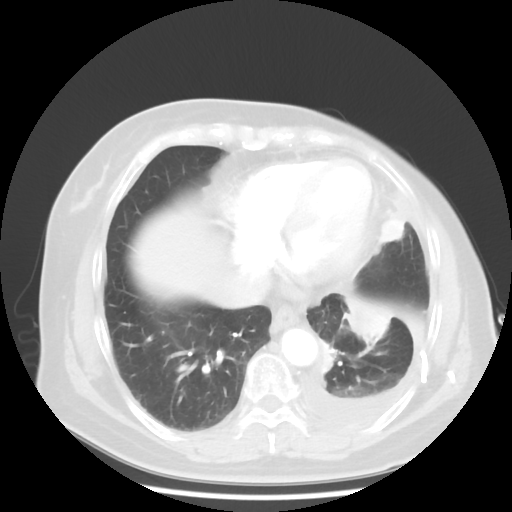
Chest CT, one axial slice; position 14 of 48 along the scan axis; 120 kVp; lung window (W 1500 / L -600 HU); 5 mm slice thickness; 512 × 512 image matrix, field of view 360 × 360 mm. Patient: female, 63 years. Case-level facts recorded for this patient, not image findings: clinical TNM (as recorded): T2 N0 M1.
Outlined on this slice (rectangle marked by the reading radiologist):
- lung tumour (recorded histology: adenocarcinoma): bounding box (x1, y1, x2, y2) in pixels: (341, 298, 402, 354)